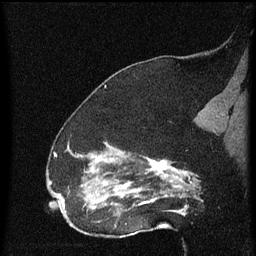
Breast MRI (dynamic contrast-enhanced), one sagittal slice; position 38 of 60 along the scan axis; dynamic contrast-enhanced series, image 2 of 4 at this slice position (ordered by acquisition); 1.5 T; TE 4.2 ms, TR 8 ms; 2 mm slice thickness; 256 × 256 image matrix. Patient: female, 52 years.
Annotated regions visible in this slice (semi-automatically segmented with operator editing):
- analysis volume of interest (the breast-tissue region the enhancement analysis was run in; not a lesion): box from (x=73, y=148) to (x=172, y=219) px
- tumour enhancement mask (voxels above the 70 % enhancement threshold inside the analysis volume of interest): (x=88, y=156)–(x=172, y=211)